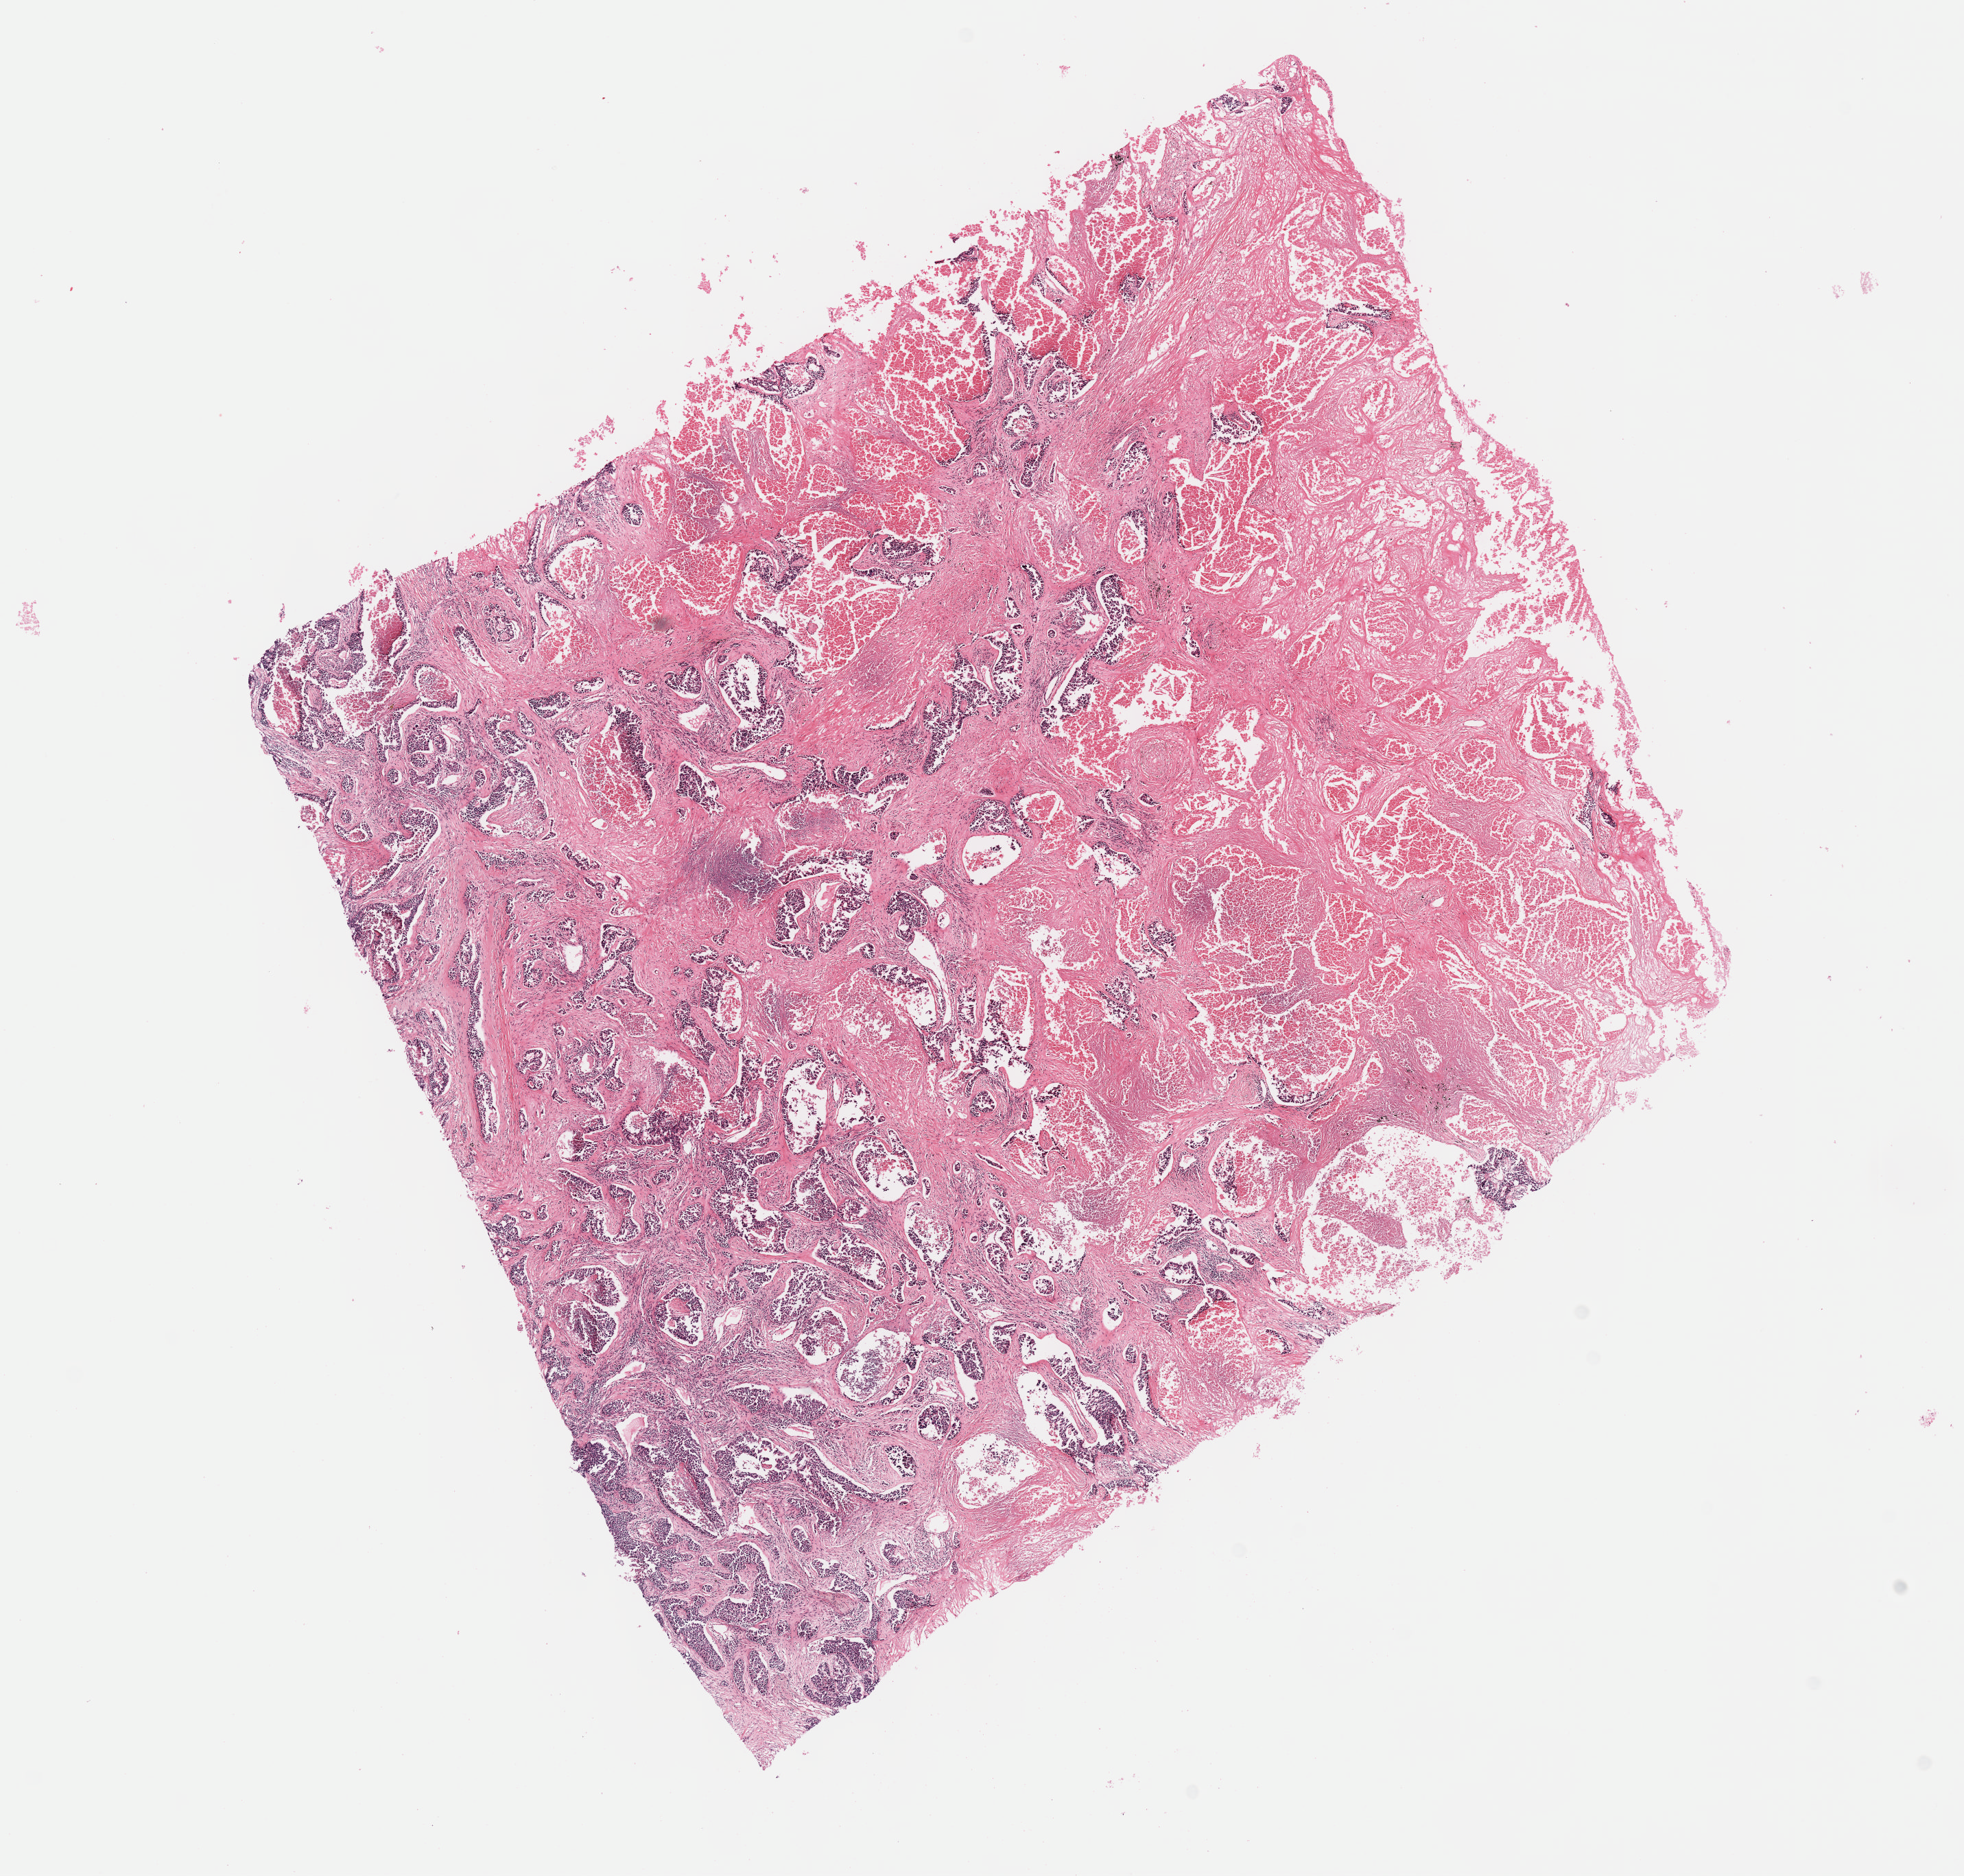
Digitized H&E tissue section (whole slide), a low-resolution overview of the entire scanned area, about 11.6 x 11.1 mm; formalin-fixed paraffin-embedded (FFPE) diagnostic section; lung, primary tumour sample. Patient: female, age at initial diagnosis 70 years.
• pathologic diagnosis: Adenocarcinoma, NOS (upper lobe, lung)